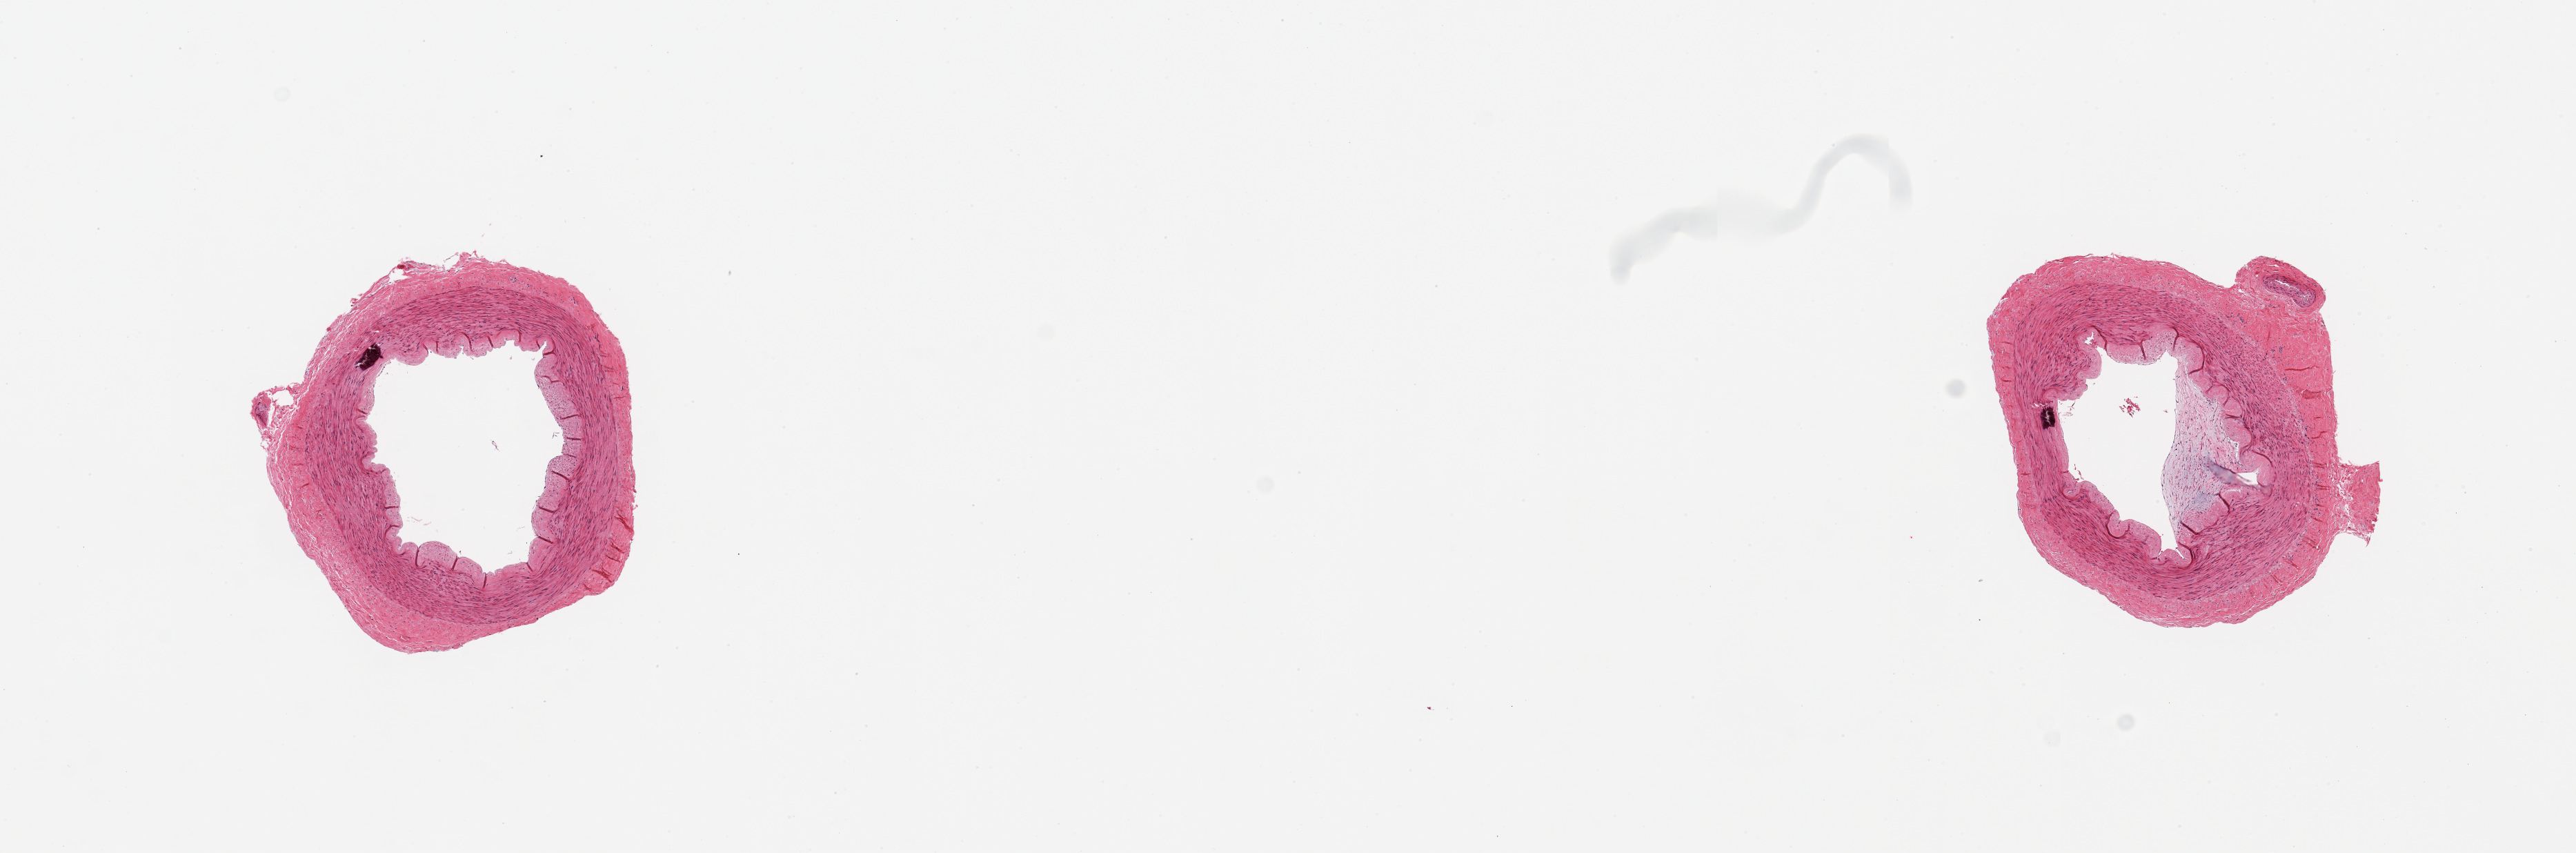
Whole-slide image, hematoxylin and eosin (H&E) stain — low-resolution overview of the scanned area, about 14.8 x 4.9 mm (from a 20x scan); PAXgene-fixed paraffin-embedded (PFPE) section; sampled site (target tissue): tibial artery; donor tissue sample. Male donor.
• reviewer comment on this tissue sample: 2 pieces; focal intimal plaque on 1; small (0.1 mm) medial calcium deposit in each; well trimmed